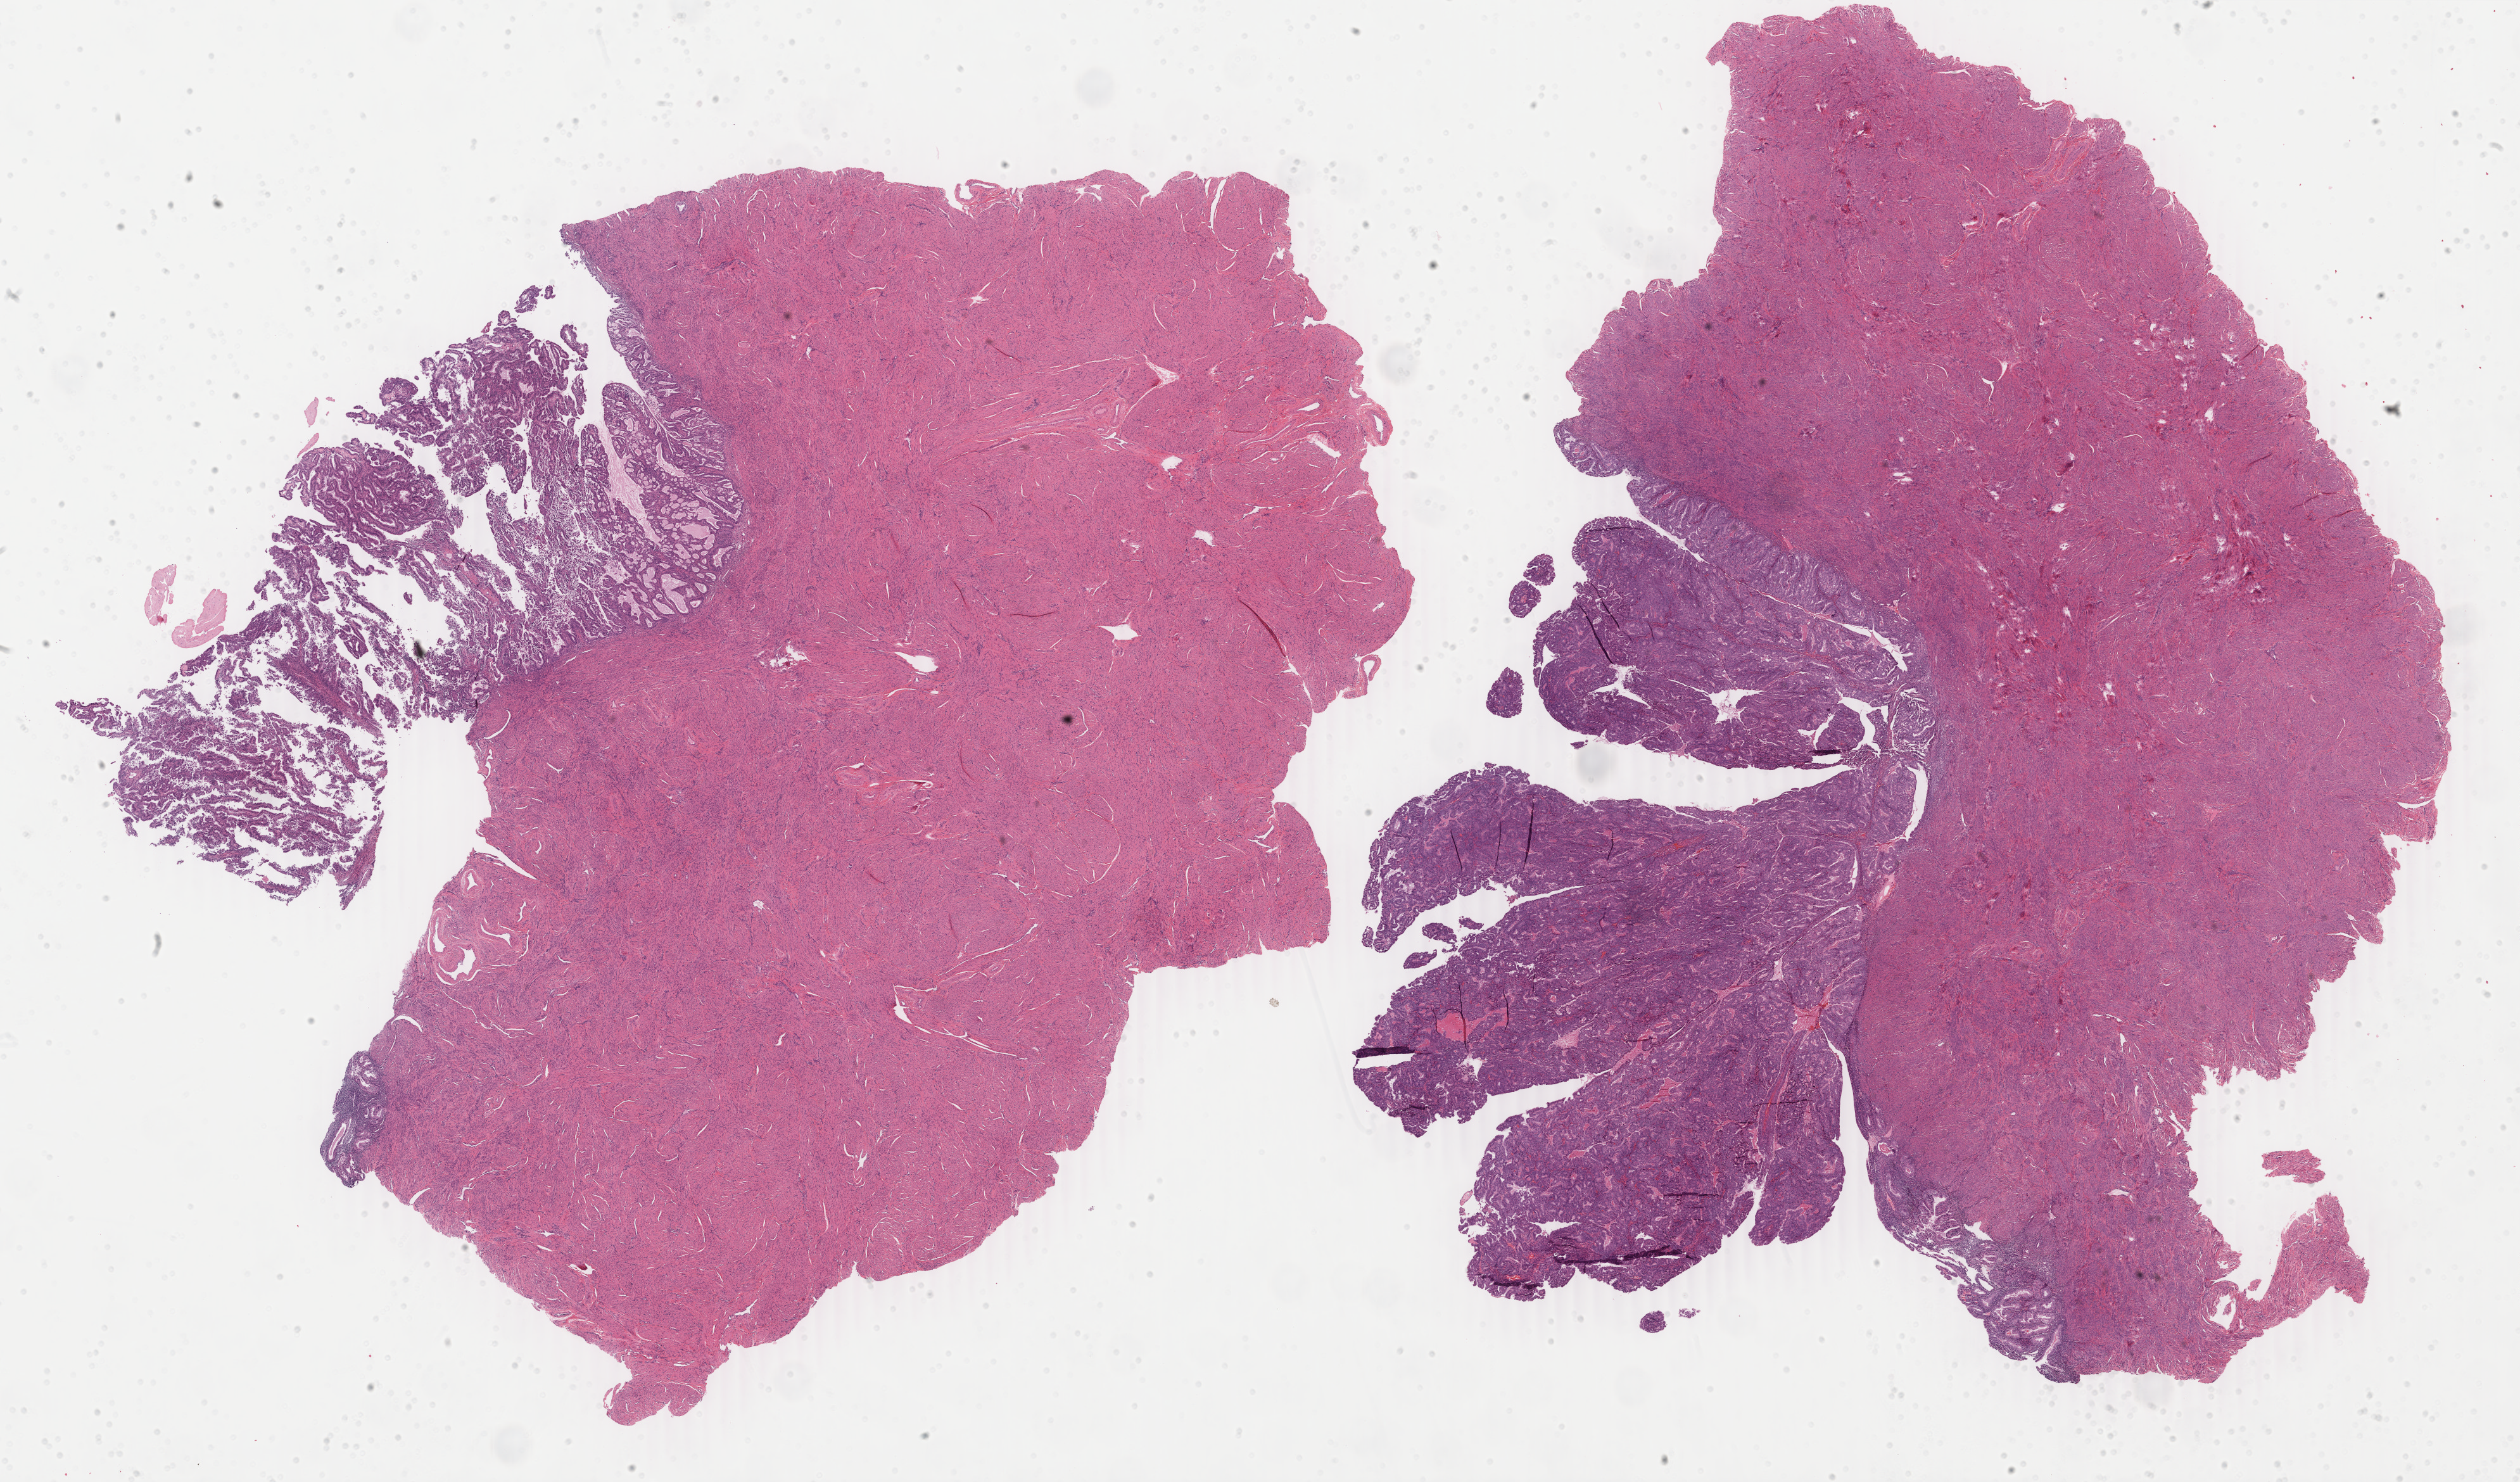
Whole-slide histology image, H&E-stained, low-resolution overview of the scanned area, about 31.6 x 18.6 mm (slide scanned at 40x). FFPE section. Sample: primary tumour, uterus. Patient: female, age at initial diagnosis 34 years. Histologic grade: G2 (moderately differentiated).
FIGO stage: IB. Pathologic diagnosis: Endometrioid adenocarcinoma, secretory variant (endometrium).